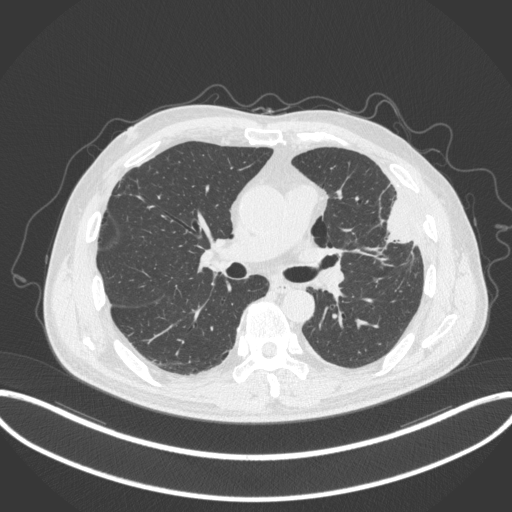
Chest CT, one axial slice; slice 191 of 382 in the series (ordered by position); 120 kVp; lung window (W 1500 / L -600 HU); 1 mm slice thickness; 512 × 512 image matrix, field of view 415 × 415 mm. Male patient, age 64 years. Case-level facts recorded for this patient, not image findings: clinical TNM (as recorded): T4 N1 M0; histopathological grade: G3.
Structures marked on this image (bounding box drawn by a radiologist):
- lung tumour (recorded histology: adenocarcinoma): bounding box [x1, y1, x2, y2] px = [373, 197, 415, 255]